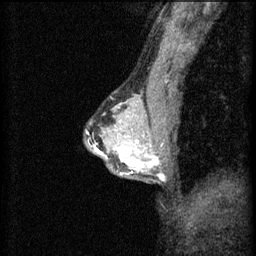
Breast MRI (dynamic contrast-enhanced), one sagittal slice. Position 39 of 60 along the scan axis. 3 images stored at this slice position (order not interpretable as contrast timing). 1.5 T. TE 4.2 ms, TR 8.2 ms. 256 × 256 image matrix, field of view 180 × 180 mm. Female patient, age 44 years.
Annotated regions visible in this slice (semi-automatically segmented with operator editing):
- analysis volume of interest (the breast-tissue region the enhancement analysis was run in; not a lesion): bounding box [x1, y1, x2, y2] px = [102, 132, 151, 181]
- tumour enhancement mask (voxels above the 70 % enhancement threshold inside the analysis volume of interest): [102, 140, 151, 173]